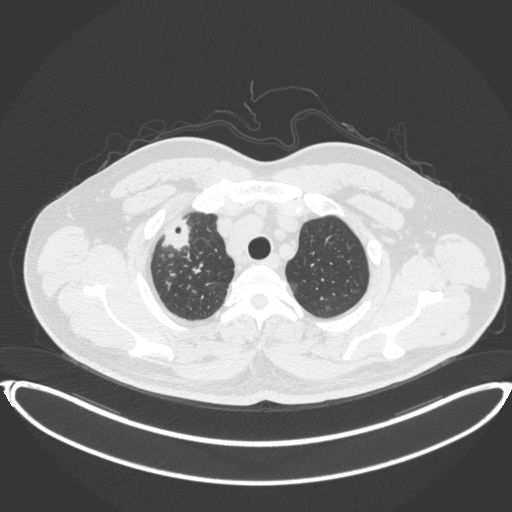
Chest CT, one axial slice. Position 334 of 399 along the scan axis. Lung window (W 1500 / L -600 HU). 512 × 512 image matrix, field of view 445 × 445 mm. Patient: male, 53 years. From the clinical record (not read from this slice): clinical TNM (as recorded): T2a N0 M0.
Outlined on this slice (rectangle marked by the reading radiologist):
- lung tumour (recorded histology: adenocarcinoma): bounding box [x1, y1, x2, y2] px = [164, 216, 195, 257]